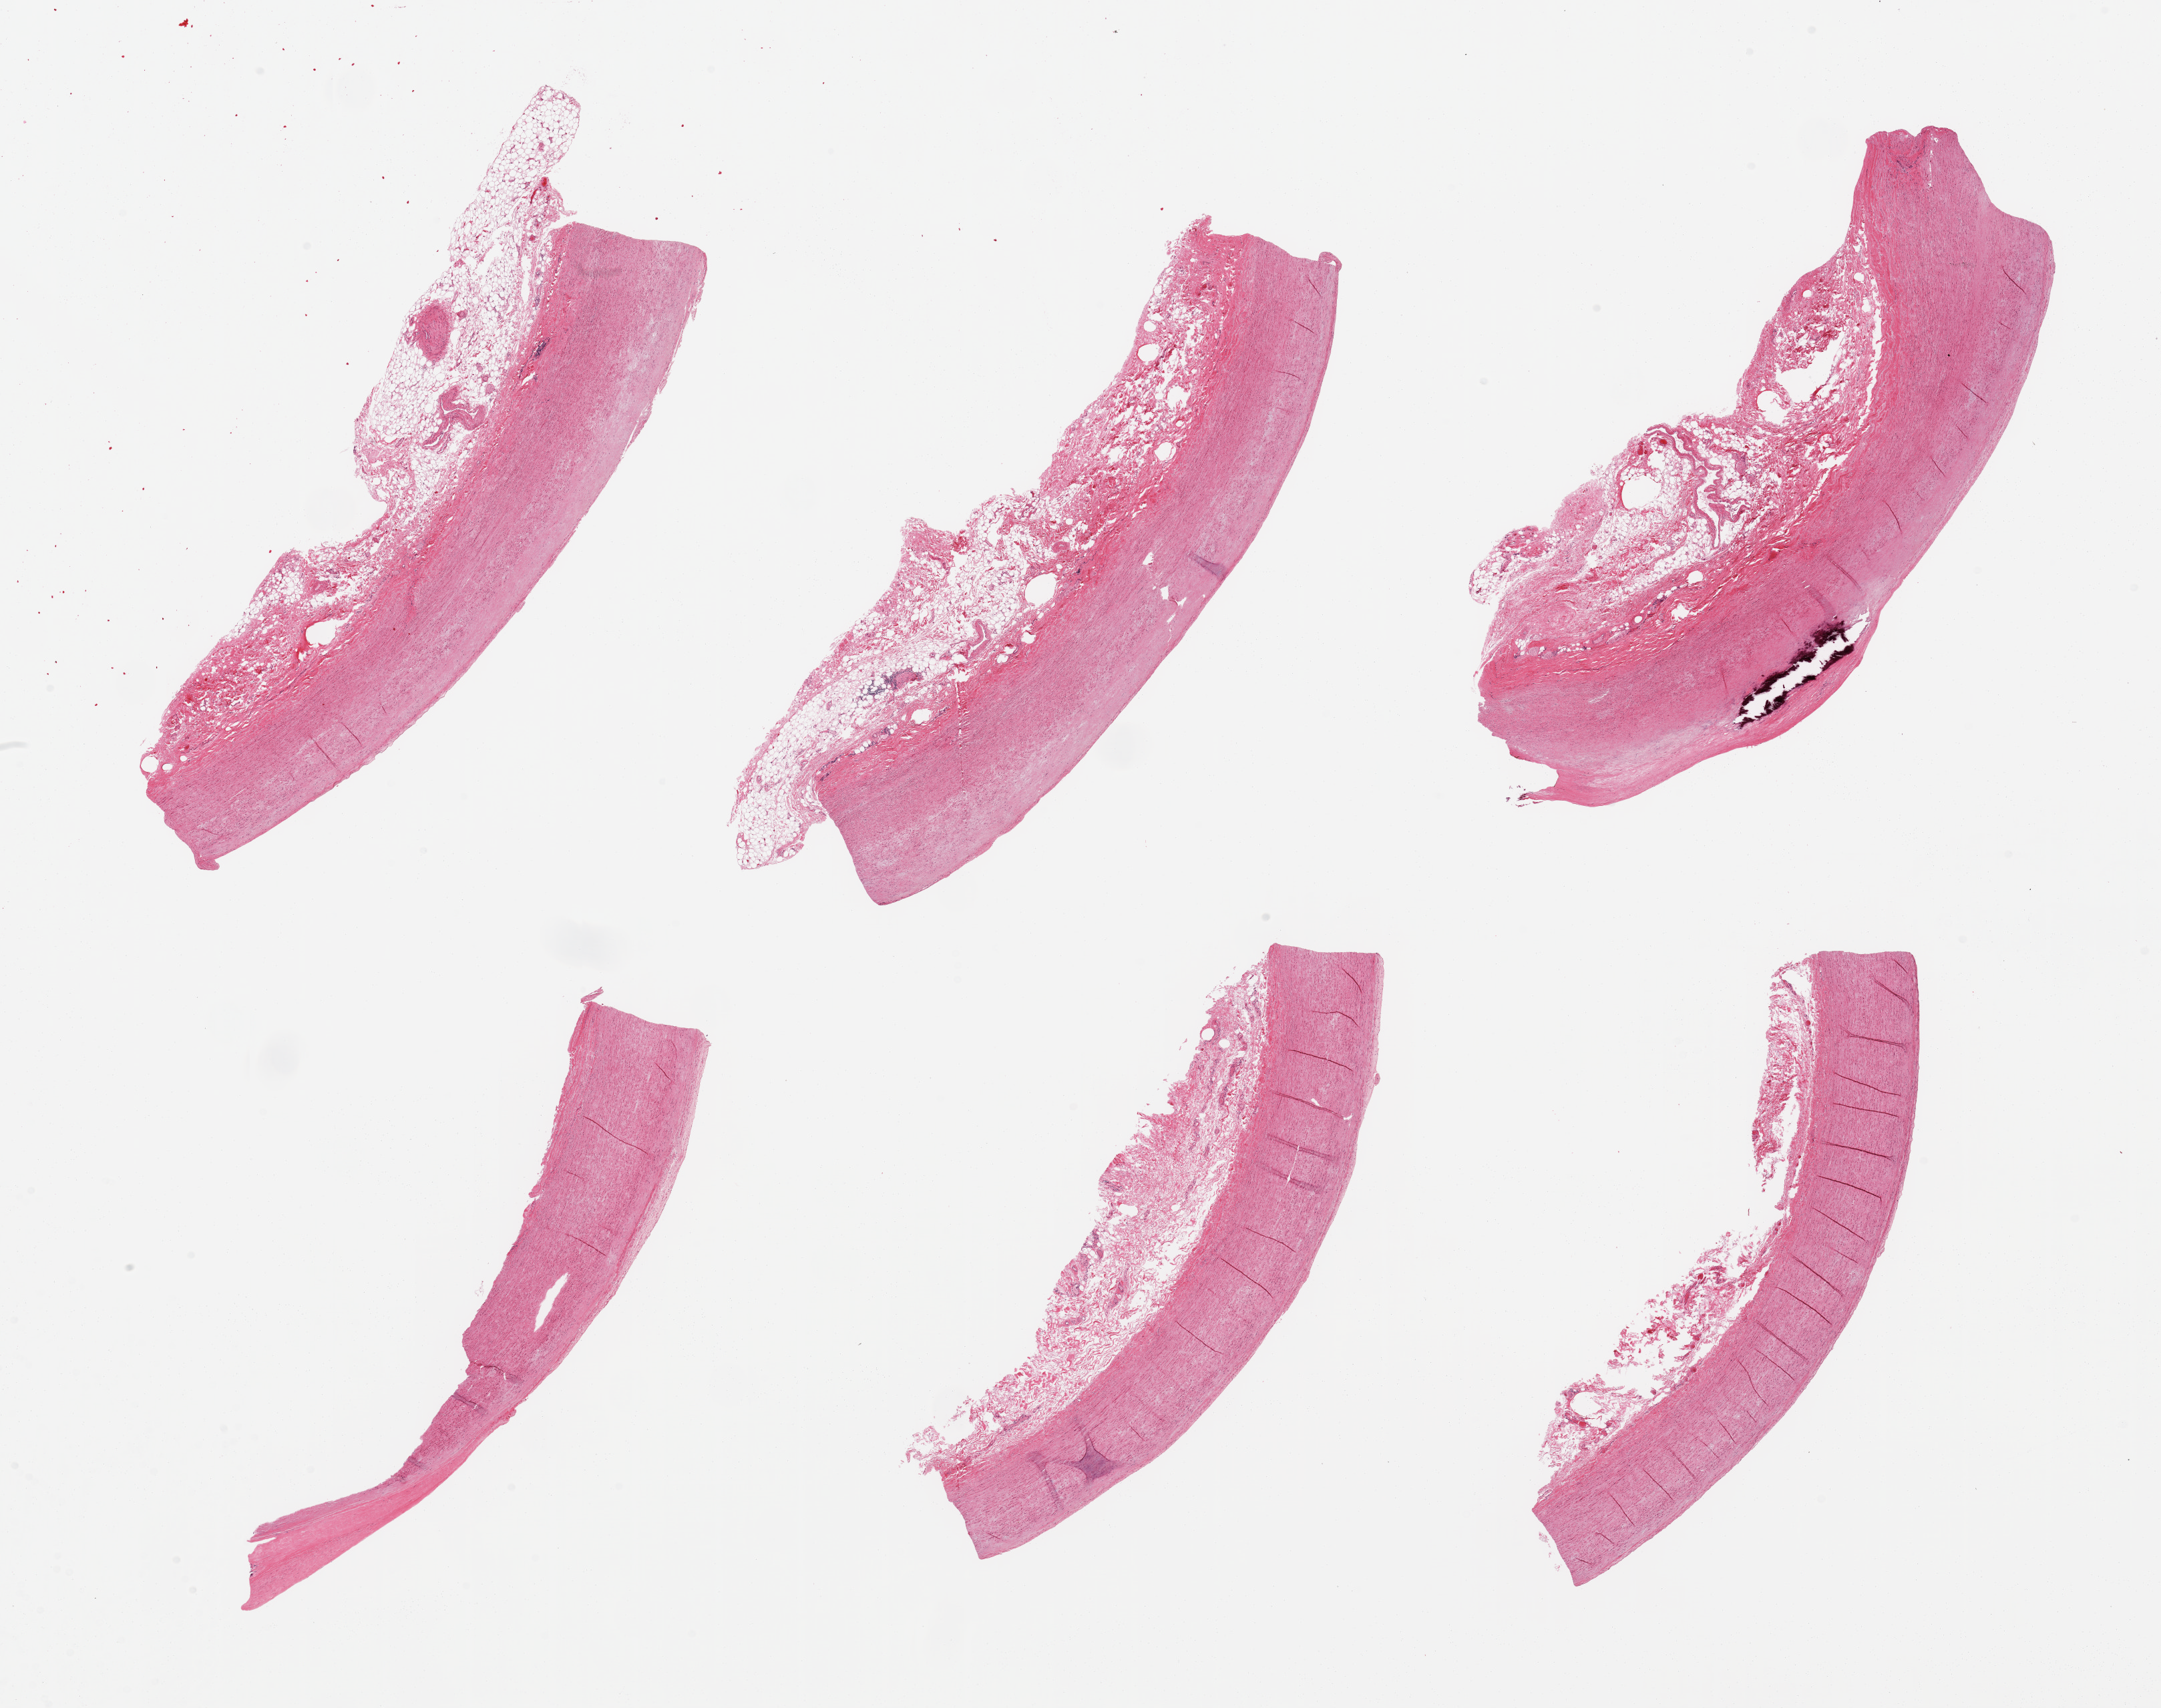
Digitized haematoxylin and eosin-stained section, brightfield, a low-resolution overview of the entire scanned area, about 25.6 x 20.2 mm (slide scanned at 20x), PAXgene-fixed paraffin-embedded (PFPE) section, sampled site (target tissue): aorta, tissue donor sample. Donor: male.
• pathologist's review note for this sample: 6 pieces, atherosis (focally calcified) up to ~0.8mm; adherent serosal fat up to ~2mm